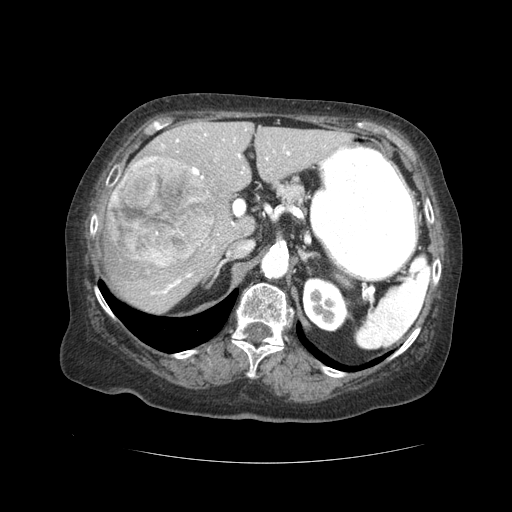
Contrast-enhanced abdominal CT (liver protocol), one axial slice; position 24 of 59 along the scan axis; soft-tissue window (W 400 / L 40 HU); 2.5 mm slice thickness; 512 × 512 image matrix, field of view 380 × 380 mm. From the clinical record (not read from this slice): diagnosis: hepatocellular carcinoma (patient treated with transarterial chemoembolisation; whether this scan precedes or follows treatment is not stated here); TNM stage (as recorded): Stage-I.
Outlined on this slice (semi-automatic segmentation, software-assisted and operator-edited):
- liver parenchyma outside the tumour (the mass and vessels are separate outlines, so this box may not span the whole liver): box from (x=104, y=120) to (x=350, y=312) px
- mass: (x=108, y=157)–(x=213, y=268)
- liver vessels: (x=151, y=134)–(x=309, y=295)